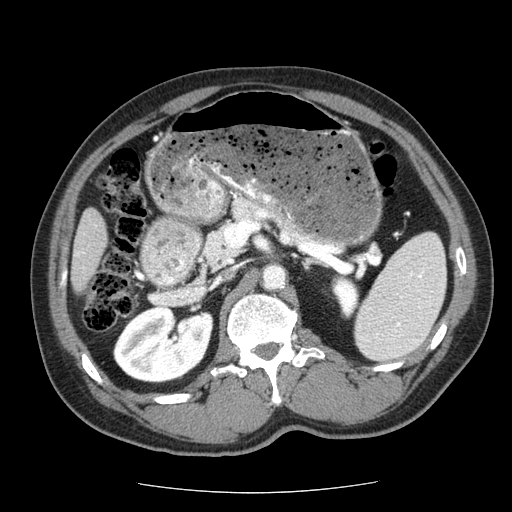
Contrast-enhanced abdominal CT (liver protocol), one axial slice. Position 16 of 85 along the scan axis. Reconstruction kernel STANDARD. 120 kVp. Soft-tissue window (W 400 / L 40 HU). 2.5 mm slice thickness. 512 × 512 image matrix, field of view 360 × 360 mm. From the clinical record (not read from this slice): diagnosis: hepatocellular carcinoma (patient treated with transarterial chemoembolisation; whether this scan precedes or follows treatment is not stated here); TNM stage (as recorded): Stage-IIIA; Child-Pugh class: A; tumour differentiation: well differentiated; tumour nodularity: multinodular.
Structures marked on this image (semi-automatically segmented with operator editing):
- liver parenchyma outside the tumour (the mass and vessels are separate outlines, so this box may not span the whole liver): box from (x=70, y=208) to (x=107, y=292) px